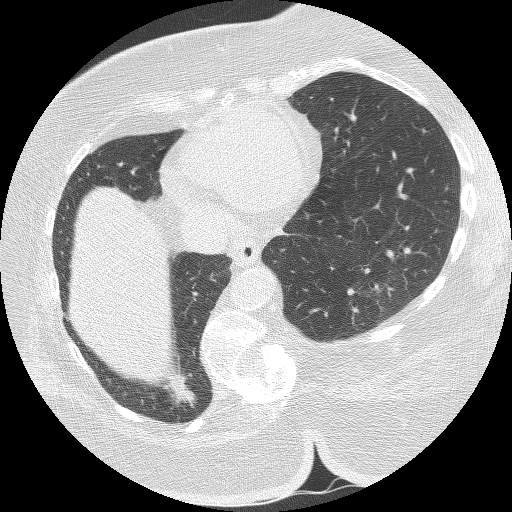
Chest CT (low-dose screening protocol), one axial image; baseline screening round; lung window (W 1500 / L -600 HU); lung (sharp) reconstruction kernel (BONE). Female, age 59 years at enrolment.
Expert-annotated lung lesion, bounding box <143,350,206,422> (left, top, right, bottom; pixels). Reader record for this screening exam (exam-level; its link to the box is not recorded): non-calcified nodule or mass ≥4 mm, right lower lobe, 21 × 10 mm, spiculated (stellate) margins, soft tissue attenuation. Later outcome: lung cancer diagnosed 52 days after this screen — bronchiolo-alveolar carcinoma, mucinous, right lower lobe, well differentiated (G1), stage IA (AJCC 6th edition), 15 mm at pathology.